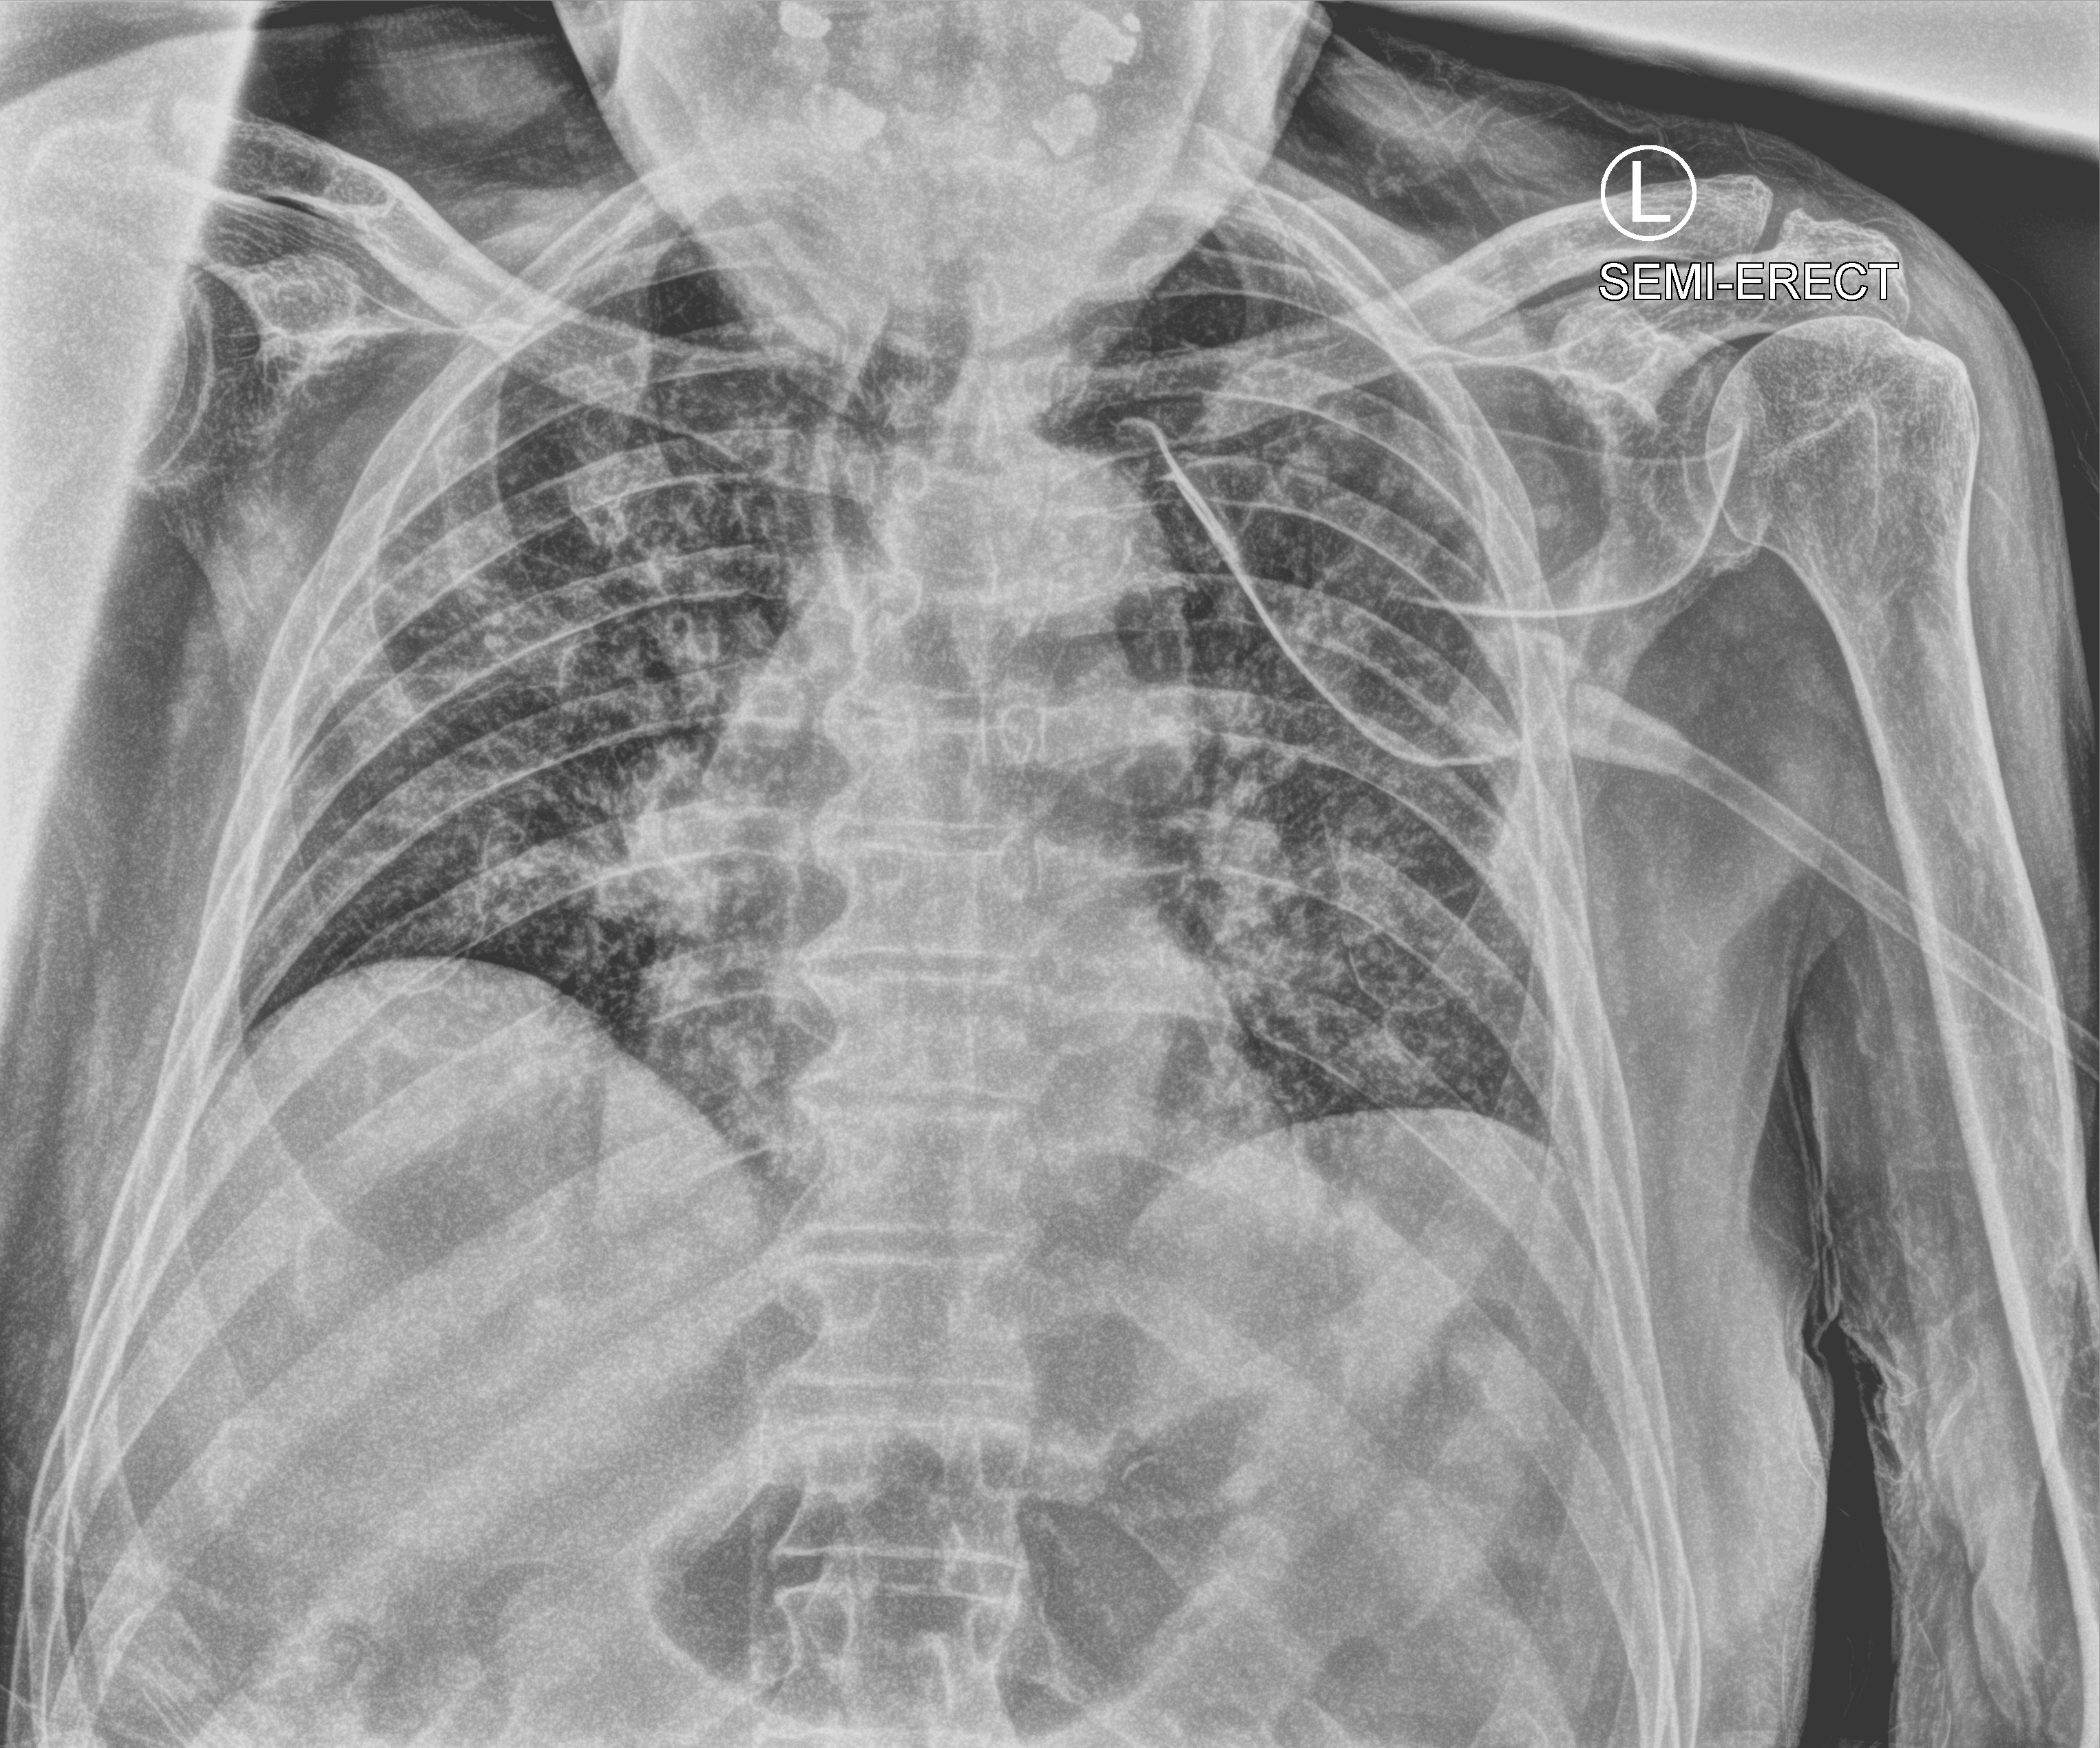
Portable chest radiograph; anteroposterior (AP) projection. Patient hospitalised with COVID-19; male, aged 75–90 years.
Admission-level facts for this patient (not findings on this image; timing relative to this image not recorded): admitted to intensive care during this hospital stay: no; mechanically ventilated during this hospital stay: no.